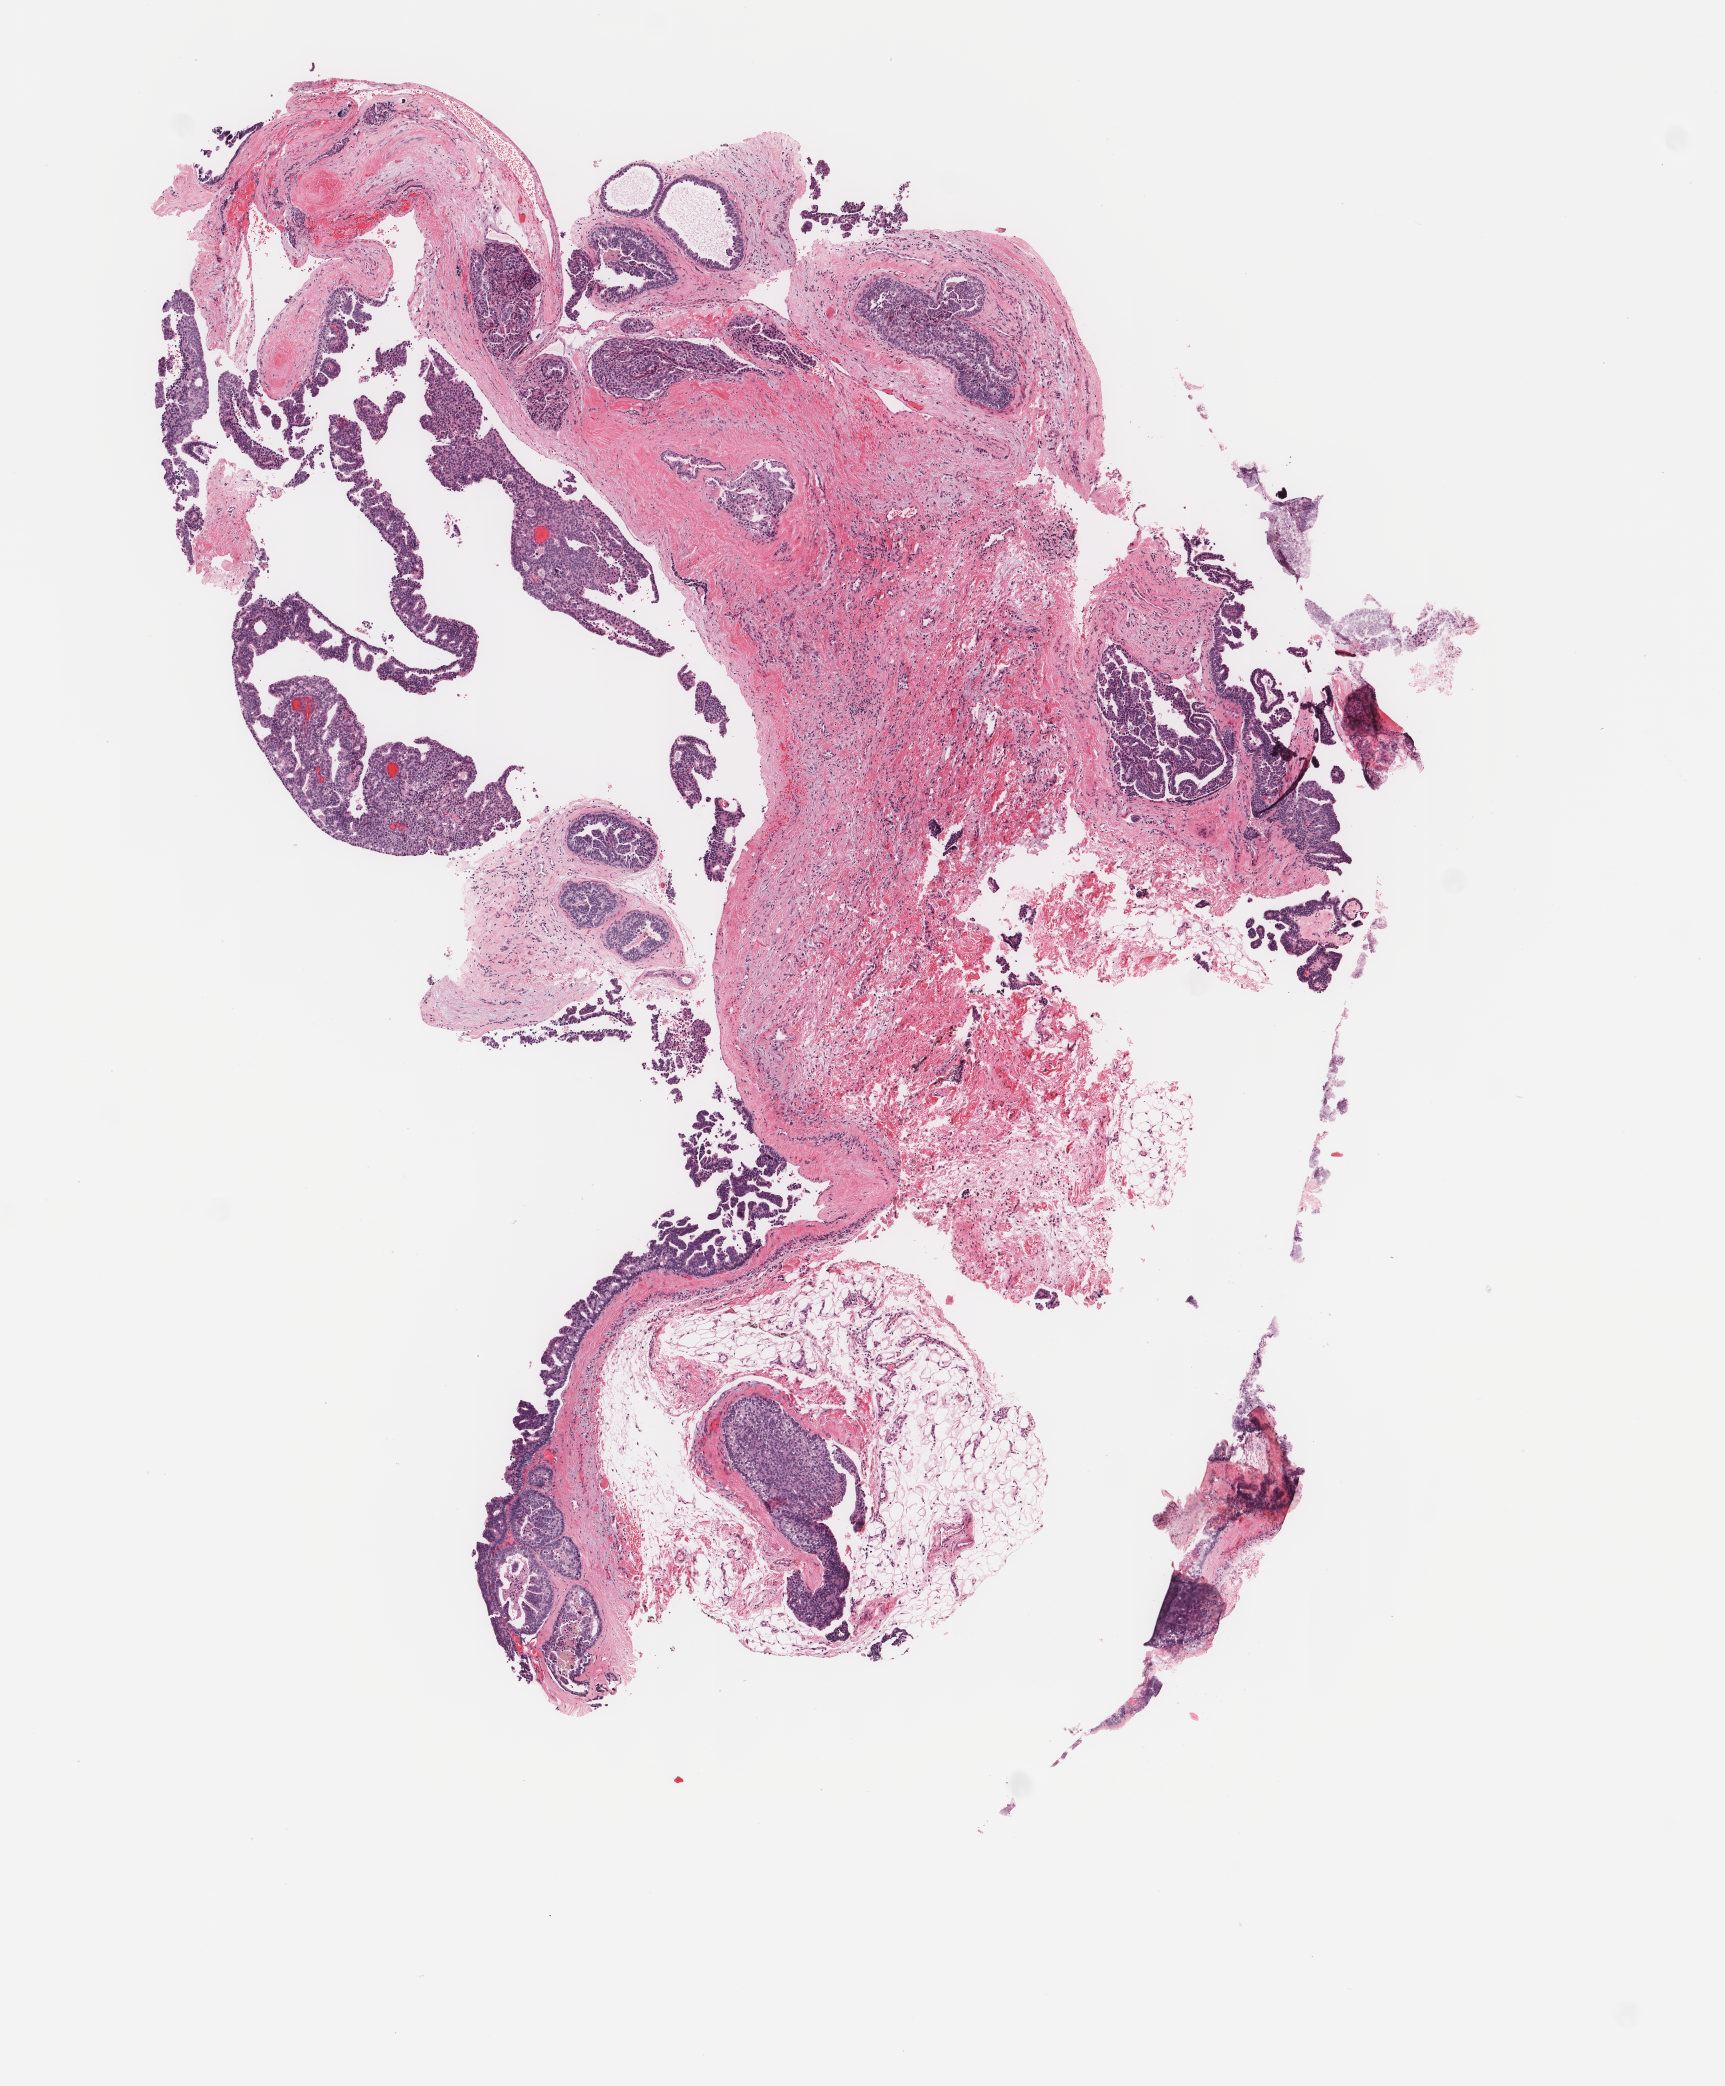
Whole-slide histology image, H&E, whole scanned area (about 6.8 x 8.3 mm, from a 40x scan) shown as a low-resolution overview; frozen section; primary tumour sample from the breast. Female, age 63 years at initial diagnosis. Slide review estimates, as recorded: tumour cells 20%, tumour nuclei 60%, normal cells 3%, stromal cells 74%, necrosis 3%. Infiltration values recorded for this section: lymphocyte infiltration 4%, monocyte infiltration 1%, neutrophil infiltration 0%.
* histologic diagnosis: Infiltrating duct carcinoma, NOS
* AJCC pathologic stage: IA